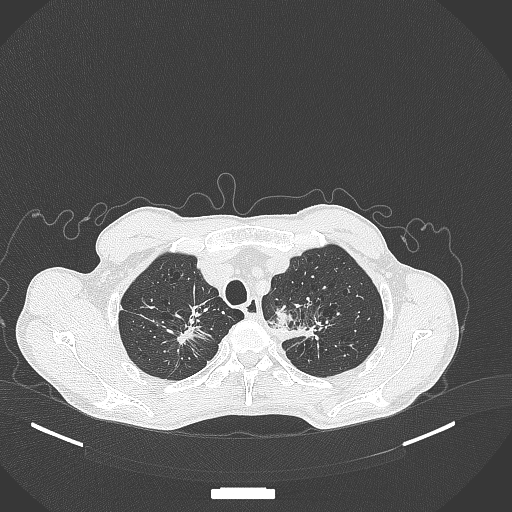
Chest CT, one axial slice; position 365 of 386 along the scan axis; 120 kVp; lung window (W 1500 / L -600 HU); 1 mm slice thickness; 512 × 512 image matrix. Male patient, age 65 years. Case-level facts recorded for this patient, not image findings: clinical TNM (as recorded): T2b N0 M0.
Structures marked on this image (rectangle marked by the reading radiologist):
- lung tumour (recorded histology: adenocarcinoma): box from (x=269, y=297) to (x=300, y=330) px